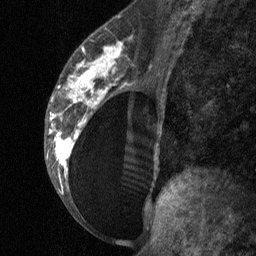
Breast MRI (dynamic contrast-enhanced), one sagittal slice. Position 35 of 64 along the scan axis. Dynamic contrast-enhanced study with each time point stored as its own series, time point 2 of 3 at this slice position (early post-contrast, ordered by acquisition time). 1.5 T. TE 4.8 ms, TR 27 ms. 256 × 256 image matrix. Patient: female, 34 years. Case-level facts recorded for this patient, not image findings: setting: breast cancer imaged before/during neoadjuvant chemotherapy; receptor status: HR-positive, HER2-negative.
Structures marked on this image (semi-automatic segmentation, software-assisted and operator-edited):
- analysis volume of interest (the breast-tissue region the enhancement analysis was run in; not a lesion): bounding box [x1, y1, x2, y2] px = [44, 23, 157, 197]
- tumour enhancement mask (voxels above the 90 % enhancement threshold inside the analysis volume of interest): [49, 42, 123, 176]